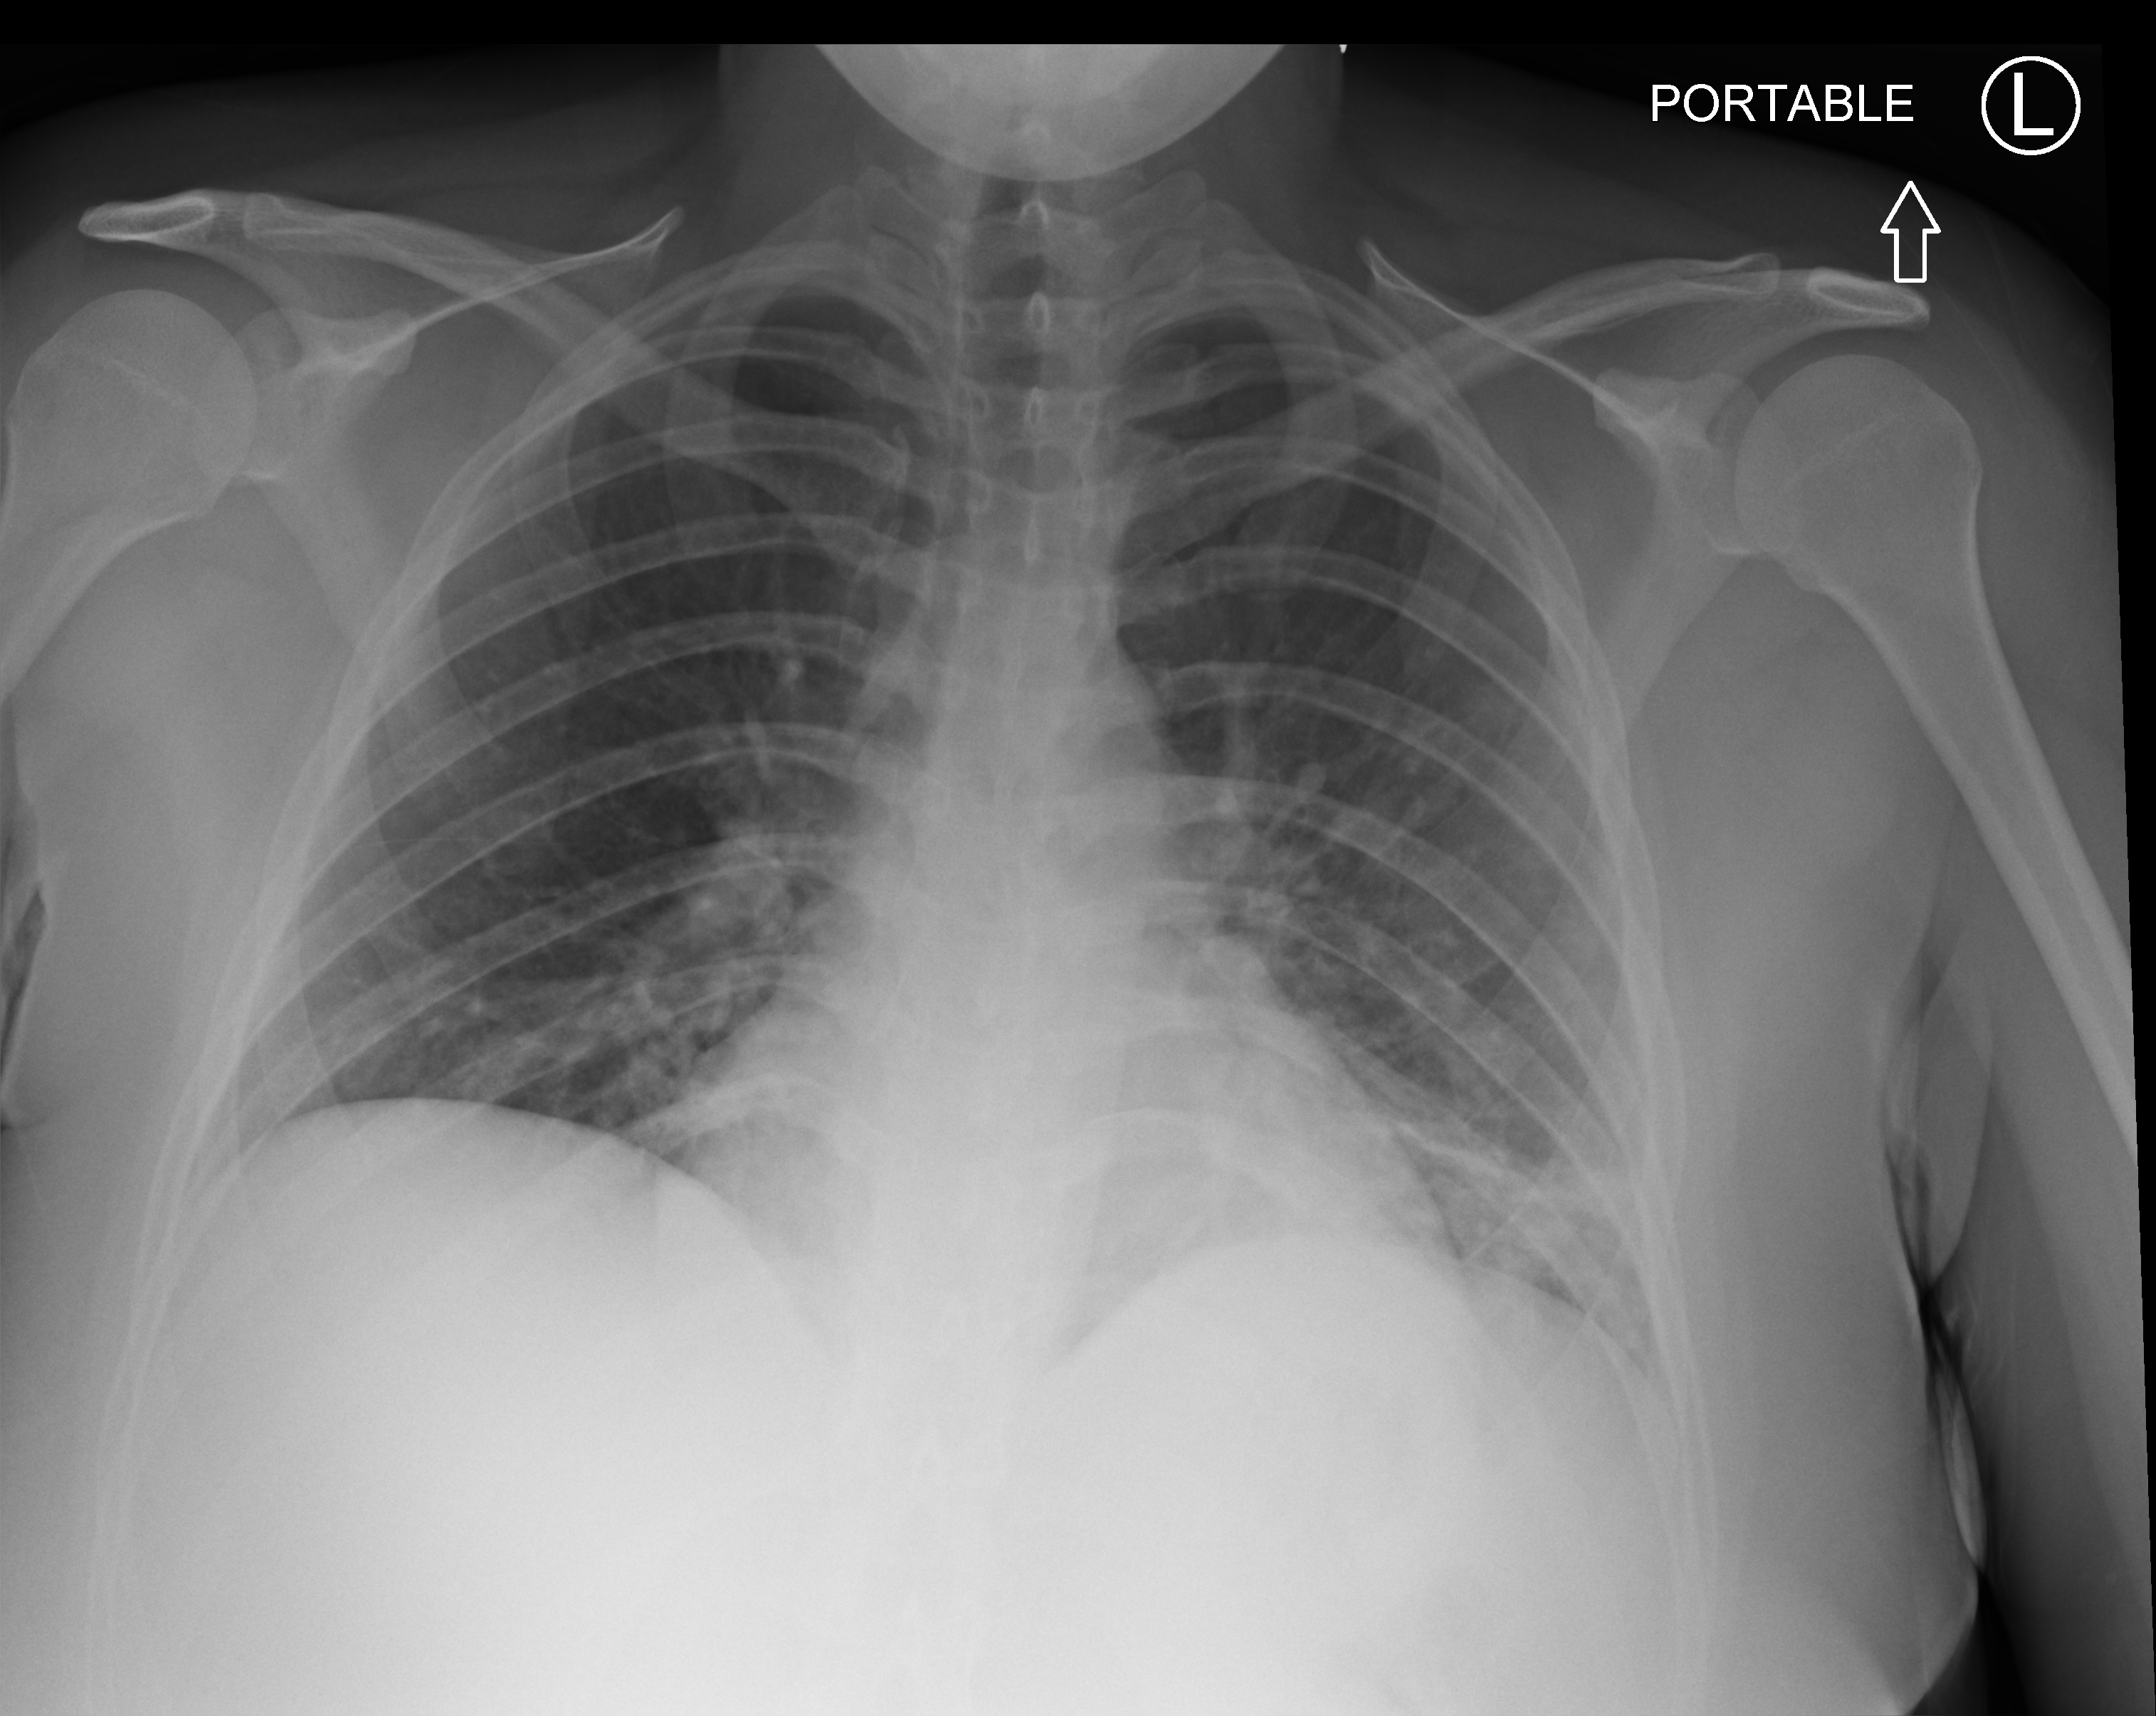
Chest X-ray (portable); anteroposterior (AP) projection. Patient hospitalised with COVID-19; female, aged 18–59 years.
From the hospital-stay record, not from the radiograph (when in the stay this image was taken is not recorded): admitted to intensive care during this hospital stay: no; hypertension (admission record): no; mechanically ventilated during this hospital stay: no.